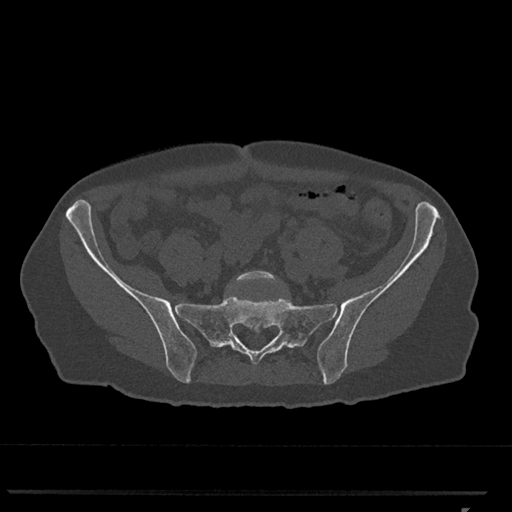
CT including the spine, one axial slice; position 106 of 793 along the scan axis; 120 kVp; bone window (W 1800 / L 400 HU); 512 × 512 image matrix, field of view 380 × 380 mm. Patient: female, 62 years. From the clinical record (not read from this slice): primary cancer: renal.
Structures marked on this image (semi-automatic segmentation, software-assisted and operator-edited):
- L5 vertebra: bounding box <235,271,278,283> (left, top, right, bottom; pixels)